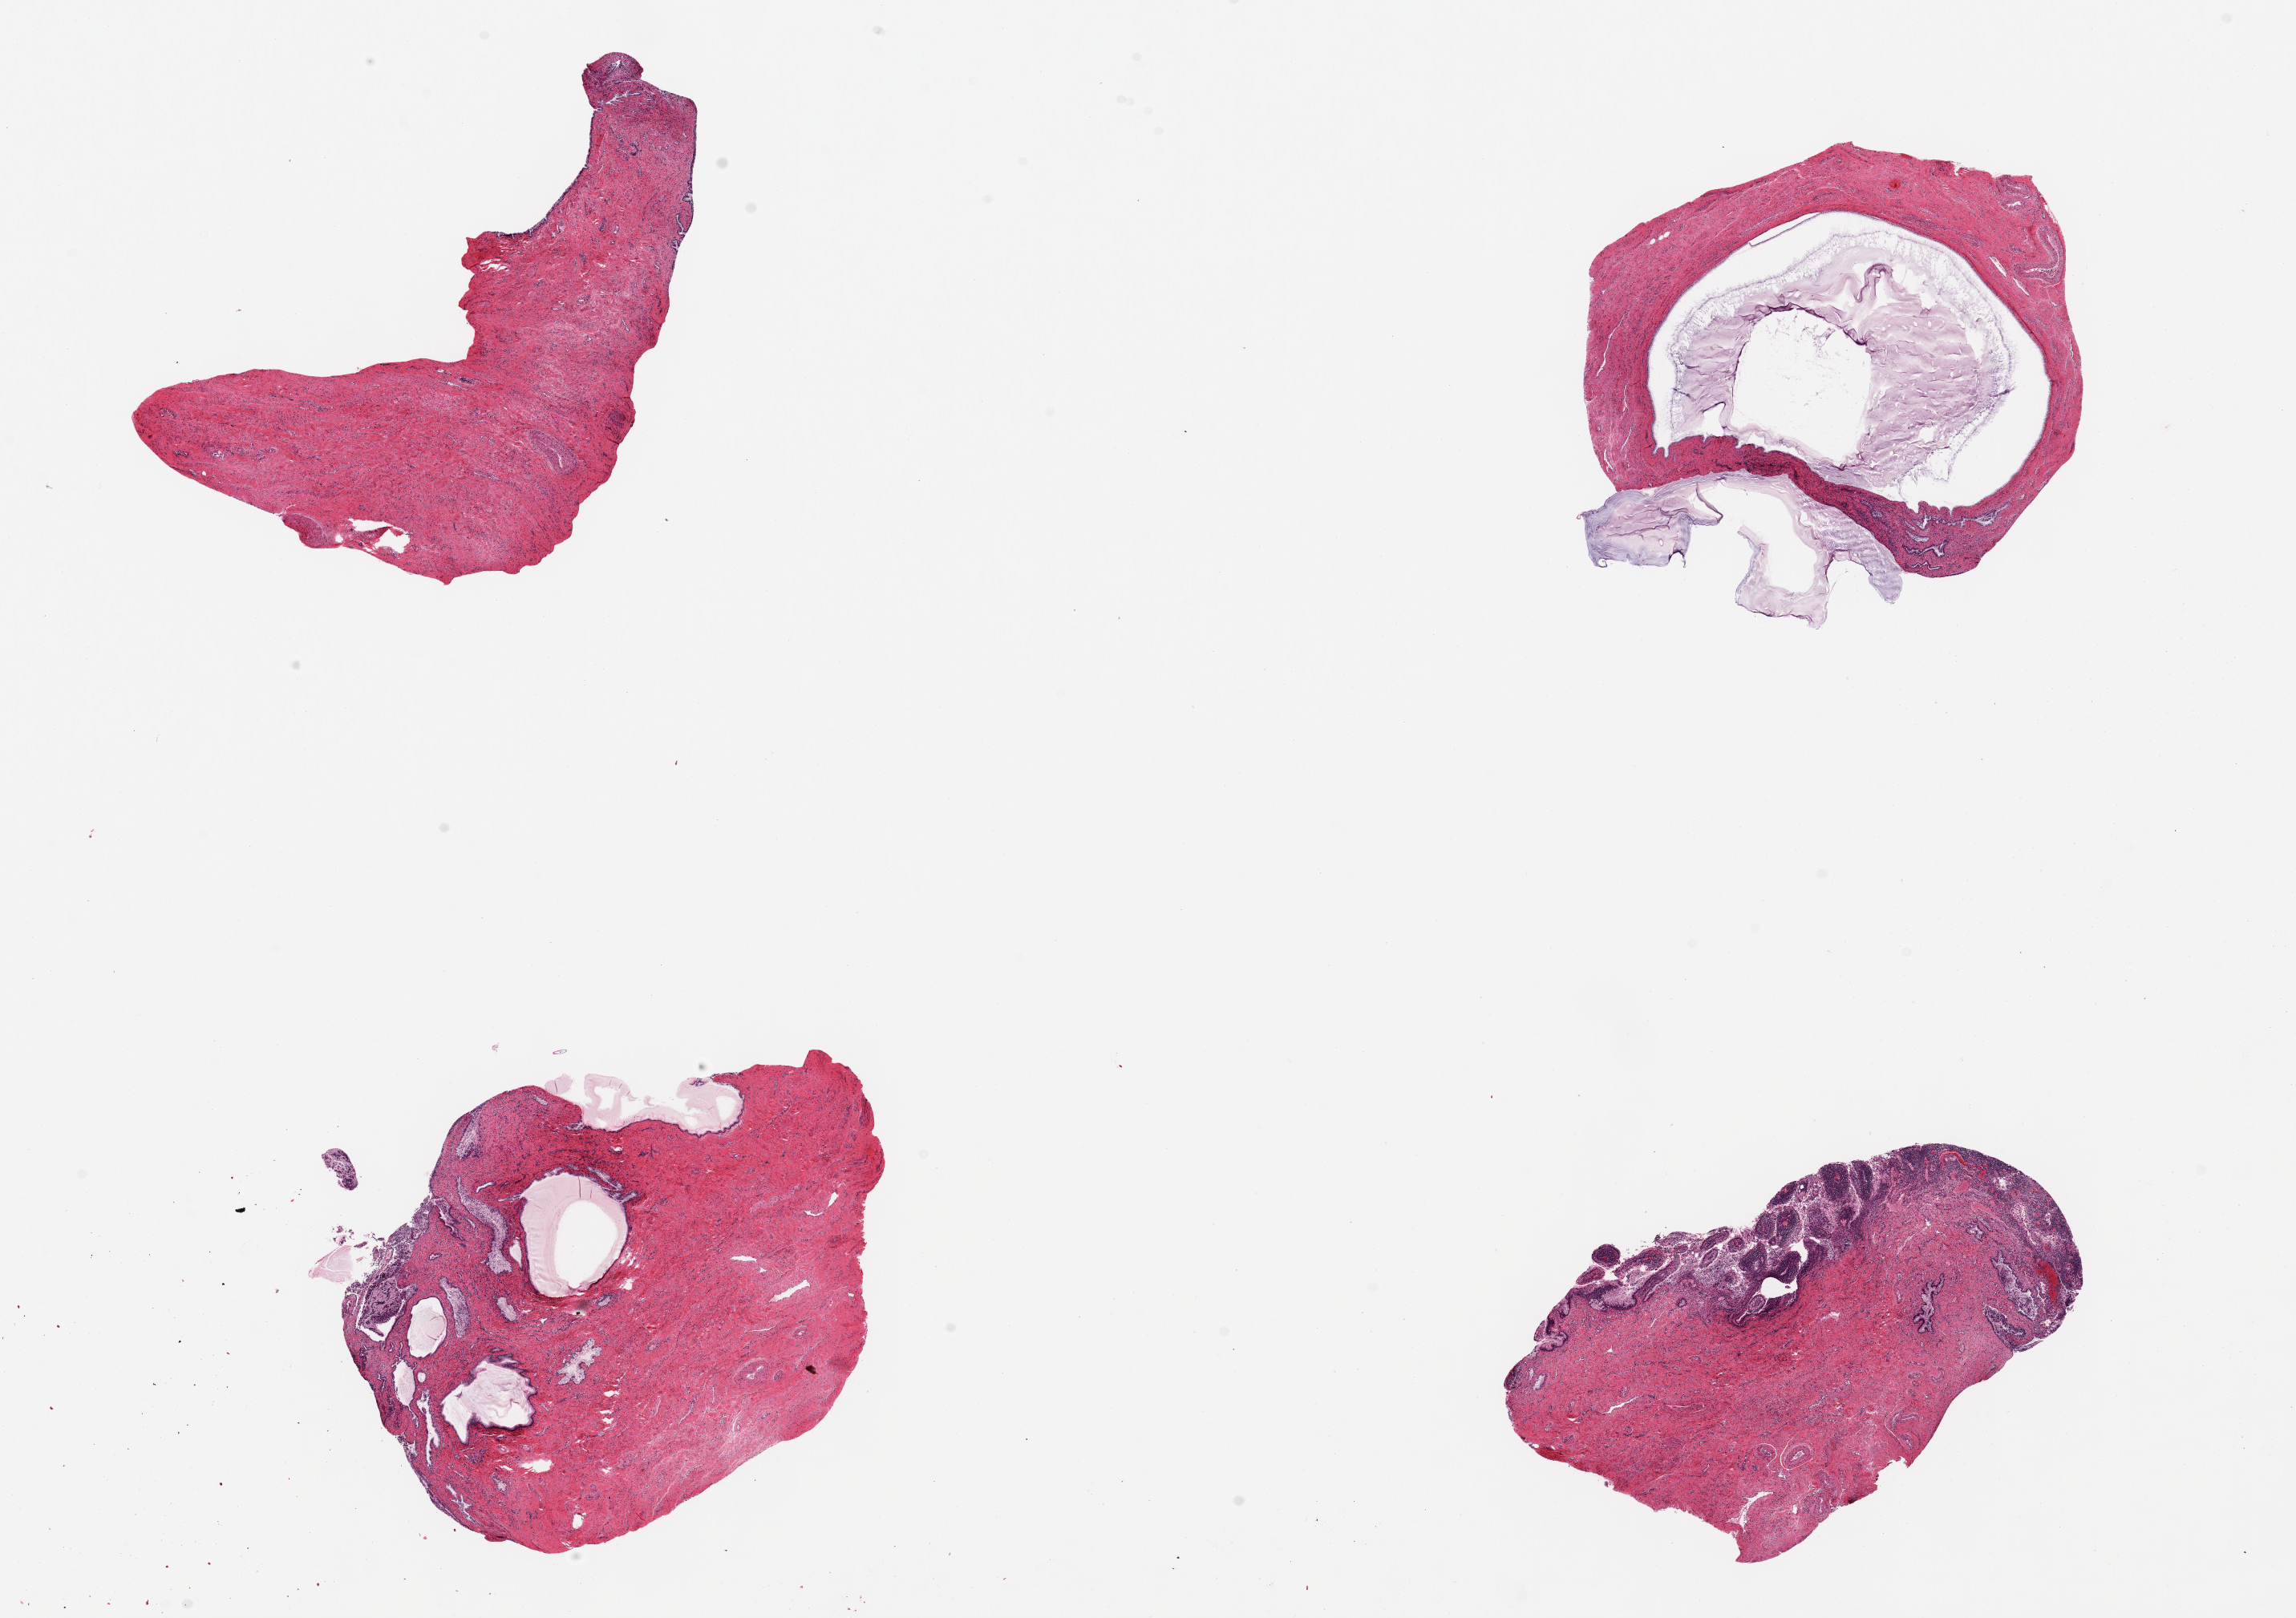
Whole-slide image, haematoxylin and eosin stain, whole scanned area (about 22.6 x 16.0 mm, acquisition: 20x scan) shown as a low-resolution overview. PAXgene-fixed, paraffin-embedded tissue. Target tissue: exocervix. Donor tissue sample. Donor sex: female.
Reviewer comment on this tissue sample: 4 ~6.5x4mm aliquots. Autolyzed endocervical glands with tunnel clusters/Nabothian cysts present.